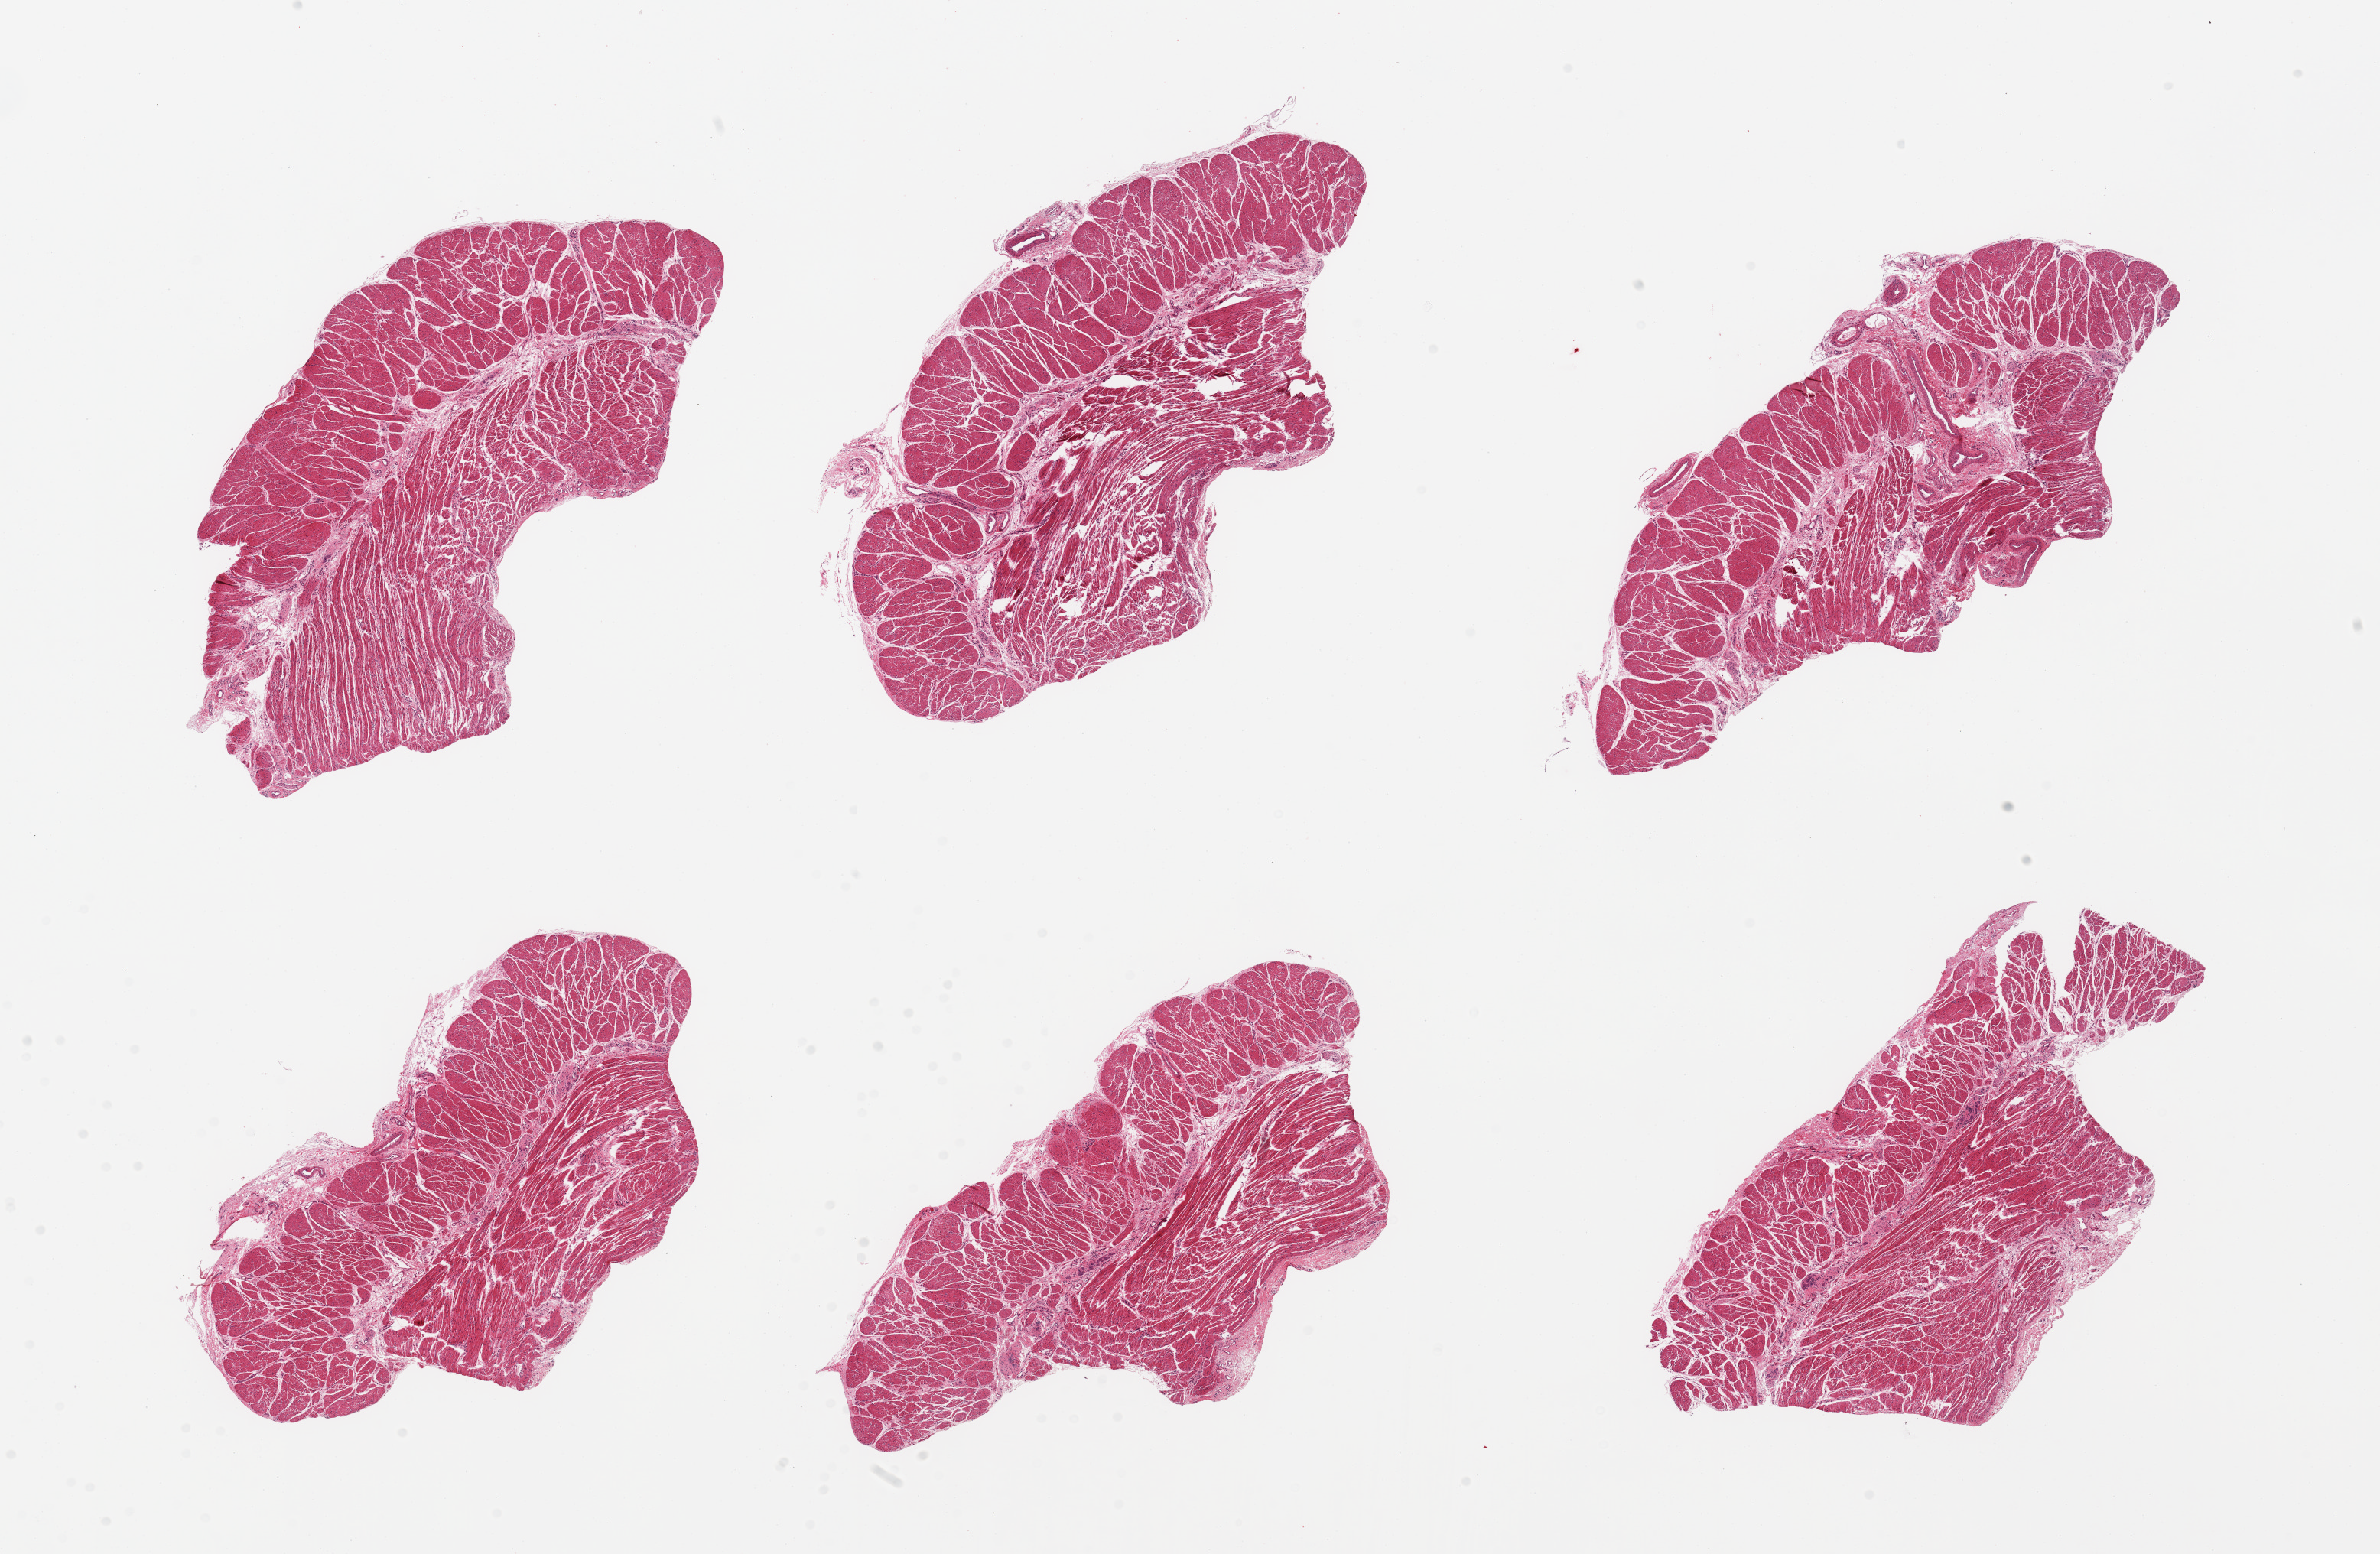
Digitized H&E-stained section — a low-resolution overview of the entire scanned area, about 24.6 x 16.1 mm (slide scanned at 20x); PAXgene-fixed, paraffin-embedded tissue; section of esophageal muscle (target tissue); donor tissue sample.
Pathologist's review note for this sample: 6 pieces, confirmed target muscularis.